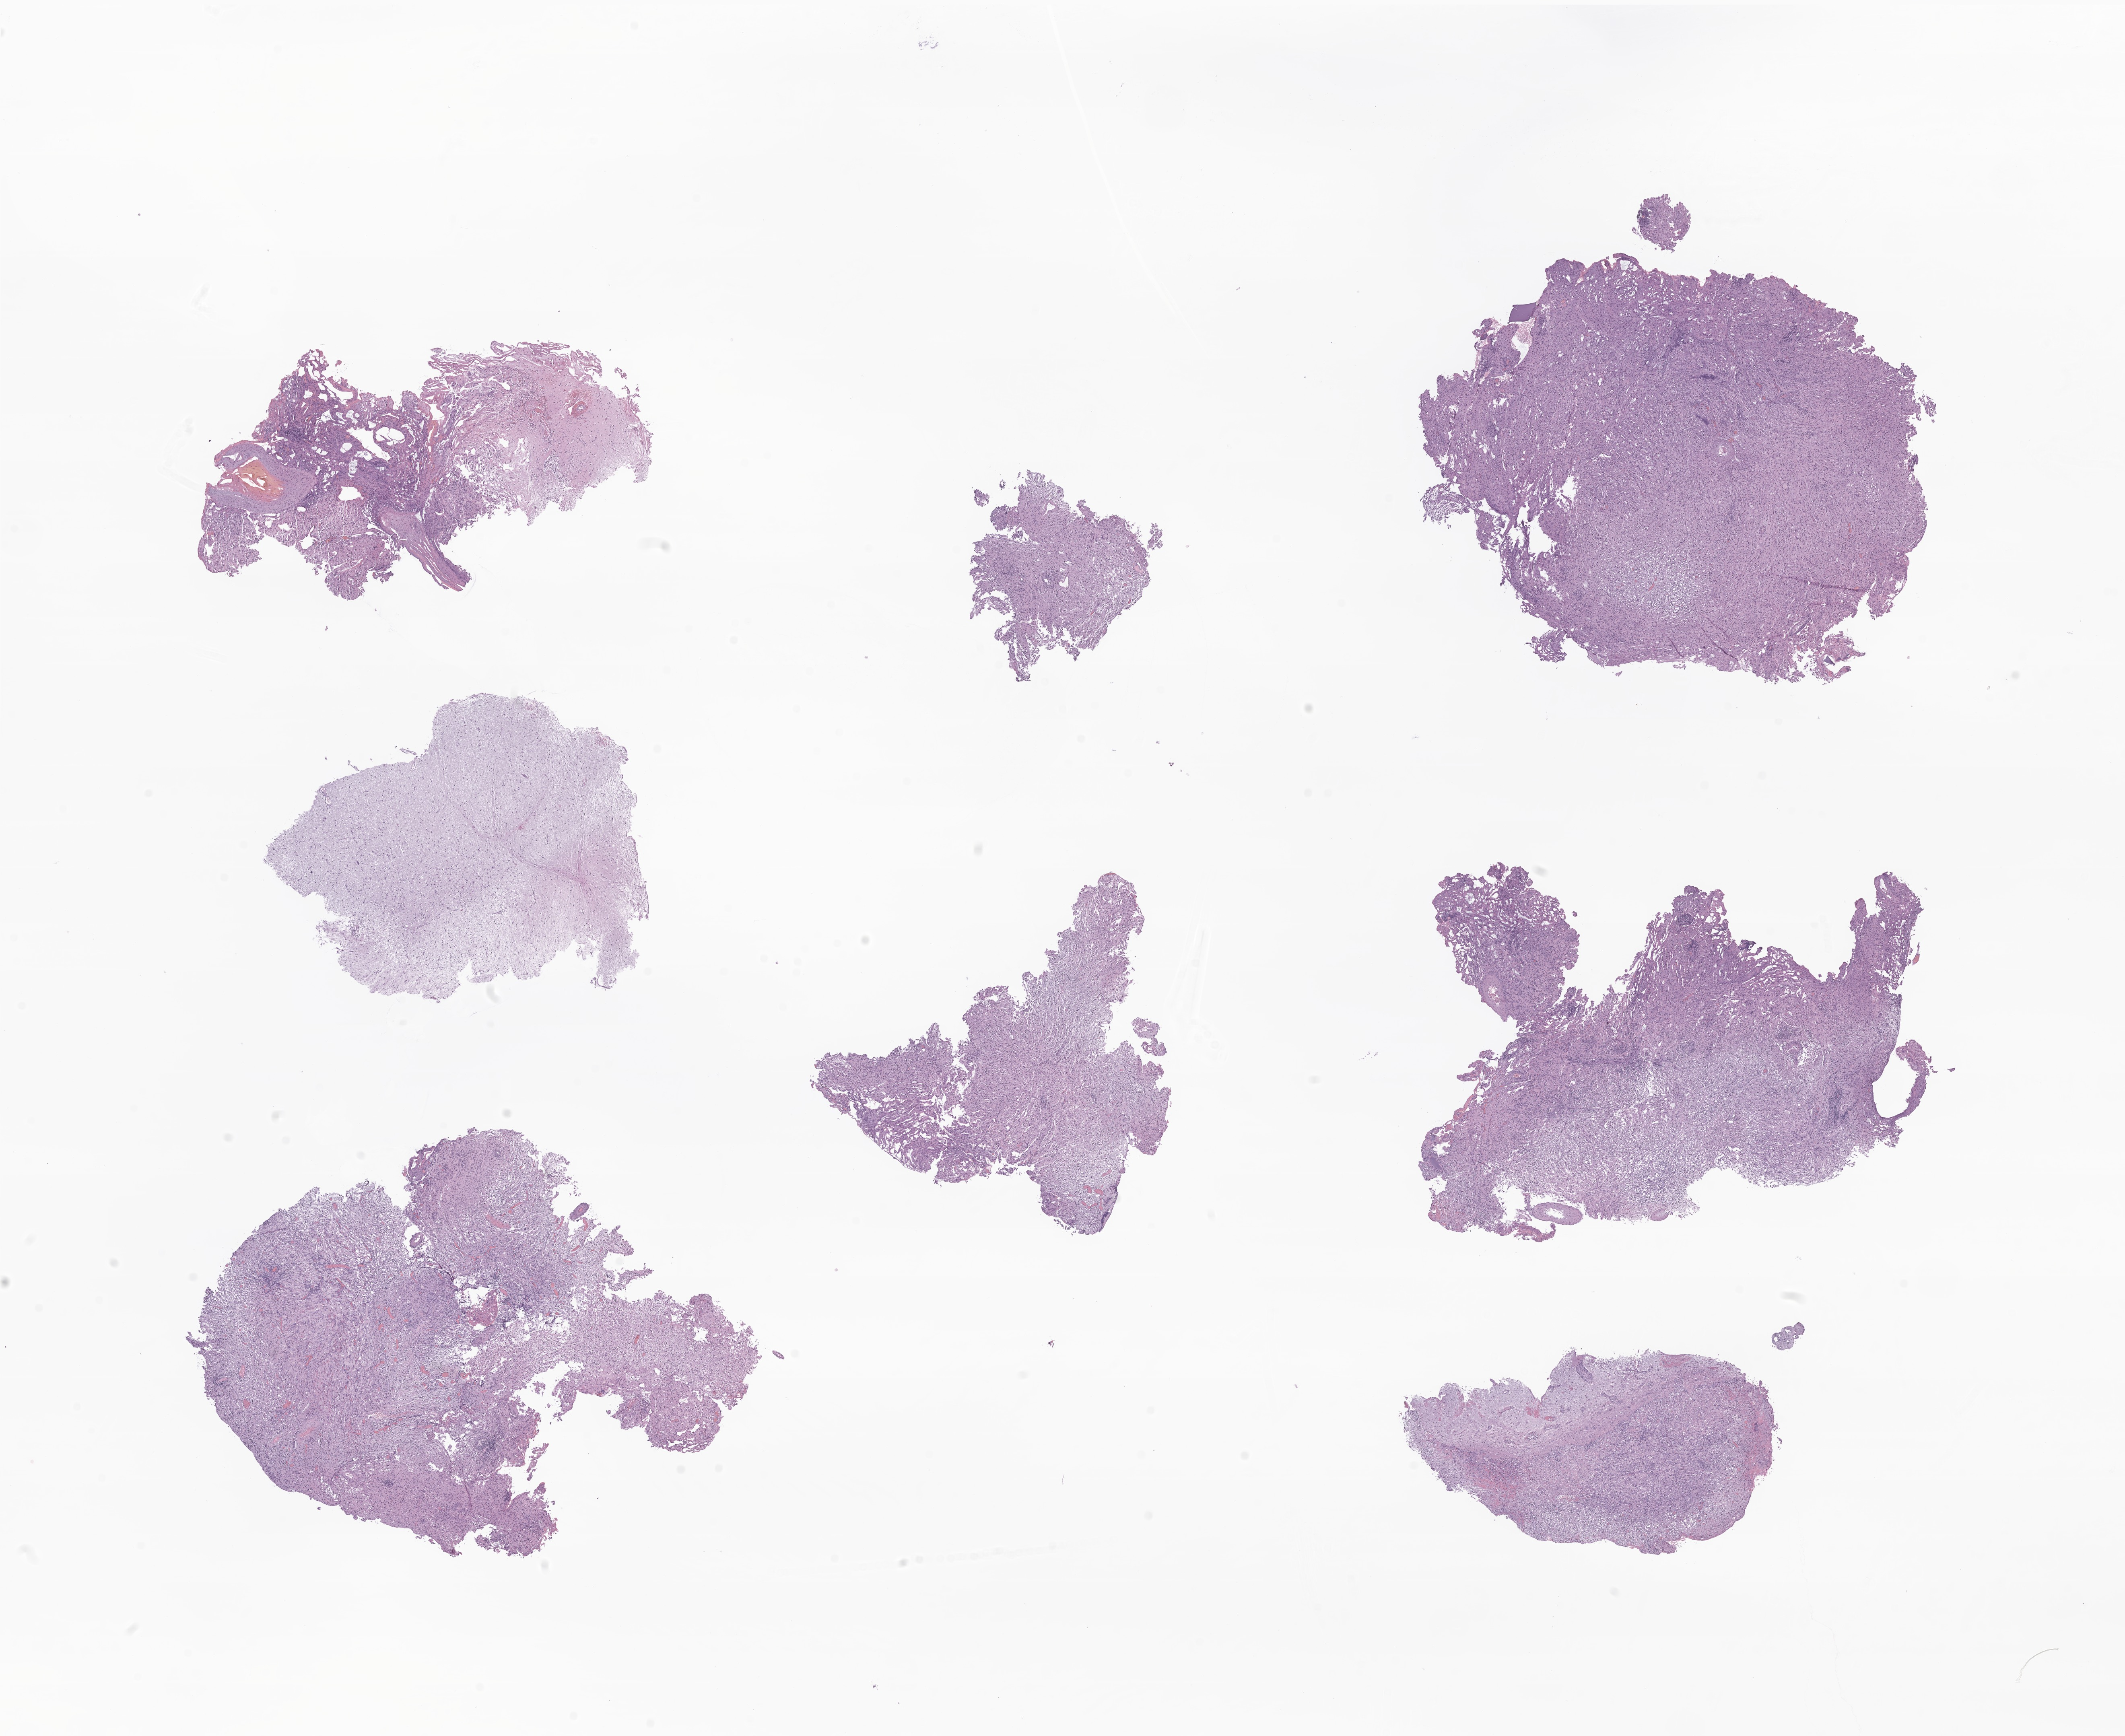
Whole-slide image, haematoxylin and eosin stain of tumor tissue from the brain — low-resolution overview of the scanned area, about 22.3 x 18.2 mm; FFPE section. Patient male; age 174 months (14 years 6 months).
• recorded diagnosis: Pleomorphic xanthoastrocytoma, NOS